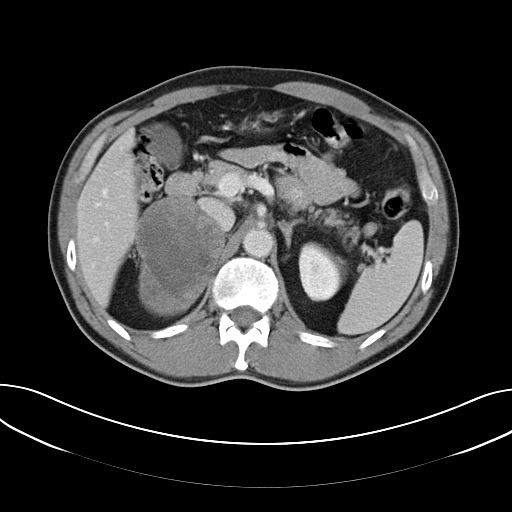
Contrast-enhanced abdominal CT, one axial slice; slice 35 of 61 in the series (ordered by position); 120 kVp; intravenous contrast given; soft-tissue window (W 400 / L 40 HU); 512 × 512 image matrix, field of view 372 × 372 mm. Male patient, age 57 years. Case-level facts recorded for this patient, not image findings: diagnosis: adrenocortical carcinoma; tumour side: right adrenal; tumour size at pathology: 11.2 cm; Ki-67 index: 10 %; stage (as recorded): 3.
Outlined on this slice (semi-automatically segmented with operator editing):
- mass: bounding box (x1, y1, x2, y2) in pixels: (136, 196, 222, 314)